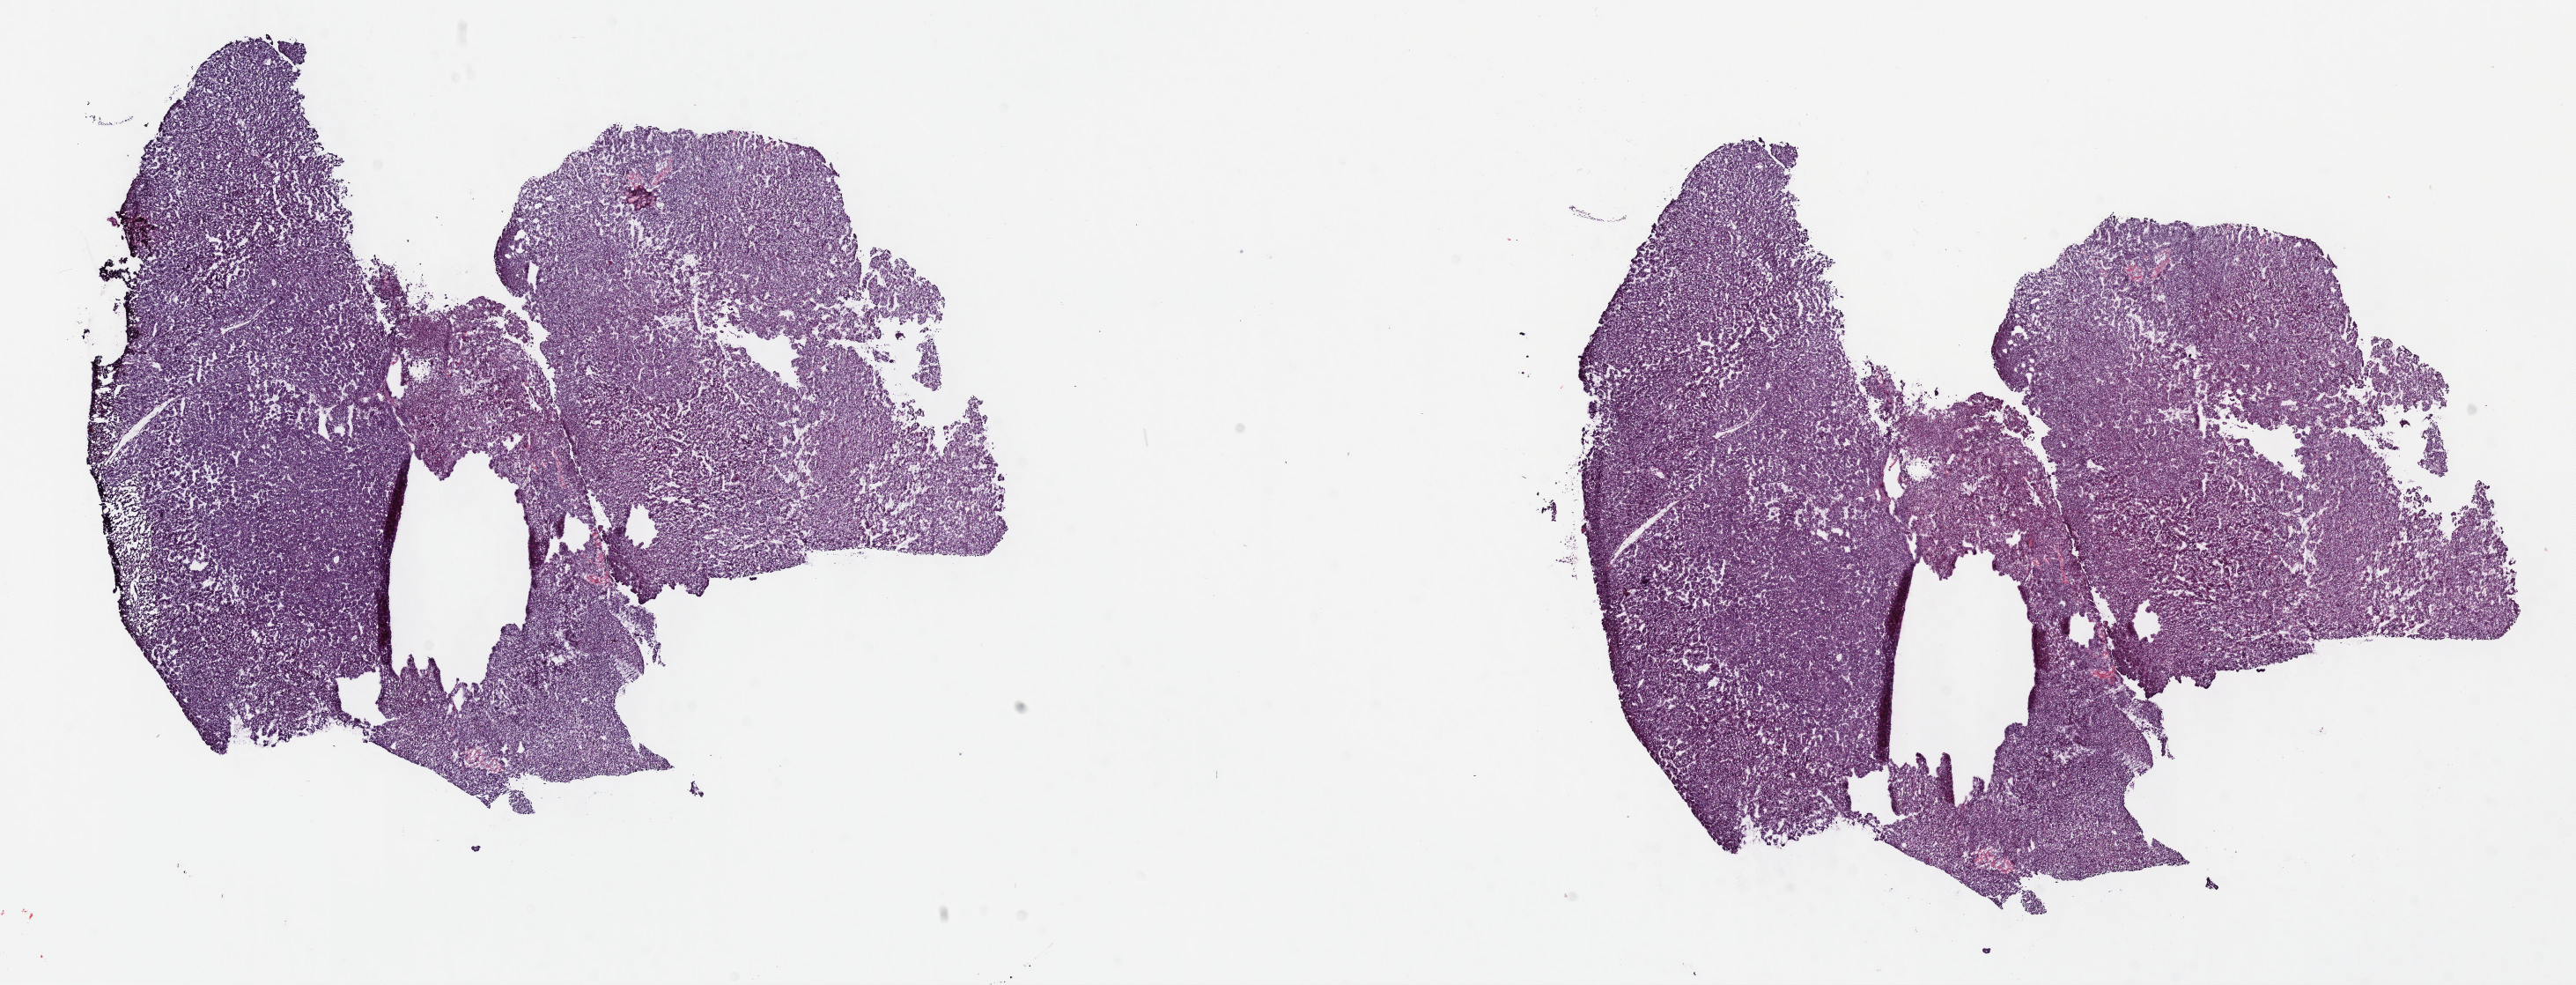
Whole-slide histology image, Hematoxylin and eosin (H&E) stained — whole scanned area (about 23.7 x 9.0 mm, slide scanned at 40x) shown as a low-resolution overview. Frozen section from the top of the tissue portion. Primary tumour sample from the liver. Male patient; age at initial diagnosis 48 years. Histologic grade: G1 (well differentiated). Composition of this section per pathologist review: tumour cells 80%, tumour nuclei 80%, normal cells 0%, stromal cells 20%, necrosis 0%. Infiltration values recorded for this section: lymphocyte infiltration 2%, monocyte infiltration 1%, neutrophil infiltration 1%.
- histologic diagnosis: Hepatocellular carcinoma, NOS
- AJCC pathologic stage: I (6th edition)